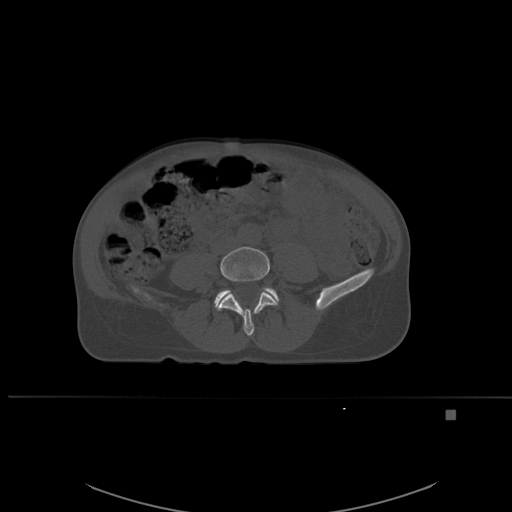
CT including the spine, one axial slice. Position 186 of 537 along the scan axis. Bone window (W 1800 / L 400 HU). 1.5 mm slice thickness. 512 × 512 image matrix, field of view 440 × 440 mm. Patient: female, 45 years. From the clinical record (not read from this slice): primary cancer: lung.
Outlined on this slice (semi-automatically segmented with operator editing):
- L4 vertebra: bounding box [x1, y1, x2, y2] px = [215, 246, 279, 336]
- L5 vertebra: [214, 287, 279, 305]